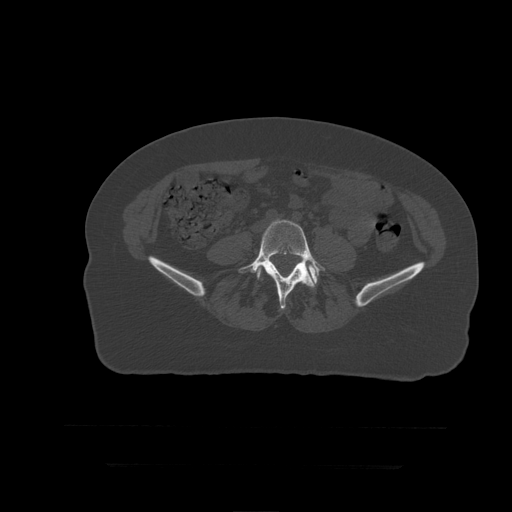
CT including the spine, one axial slice; 120 kVp; bone window (W 1800 / L 400 HU); 1.25 mm slice thickness; 512 × 512 image matrix. Patient age 41 years. From the clinical record (not read from this slice): primary cancer: breast.
Structures marked on this image (semi-automatically segmented with operator editing):
- L5 vertebra: bounding box [x1, y1, x2, y2] px = [239, 219, 326, 310]